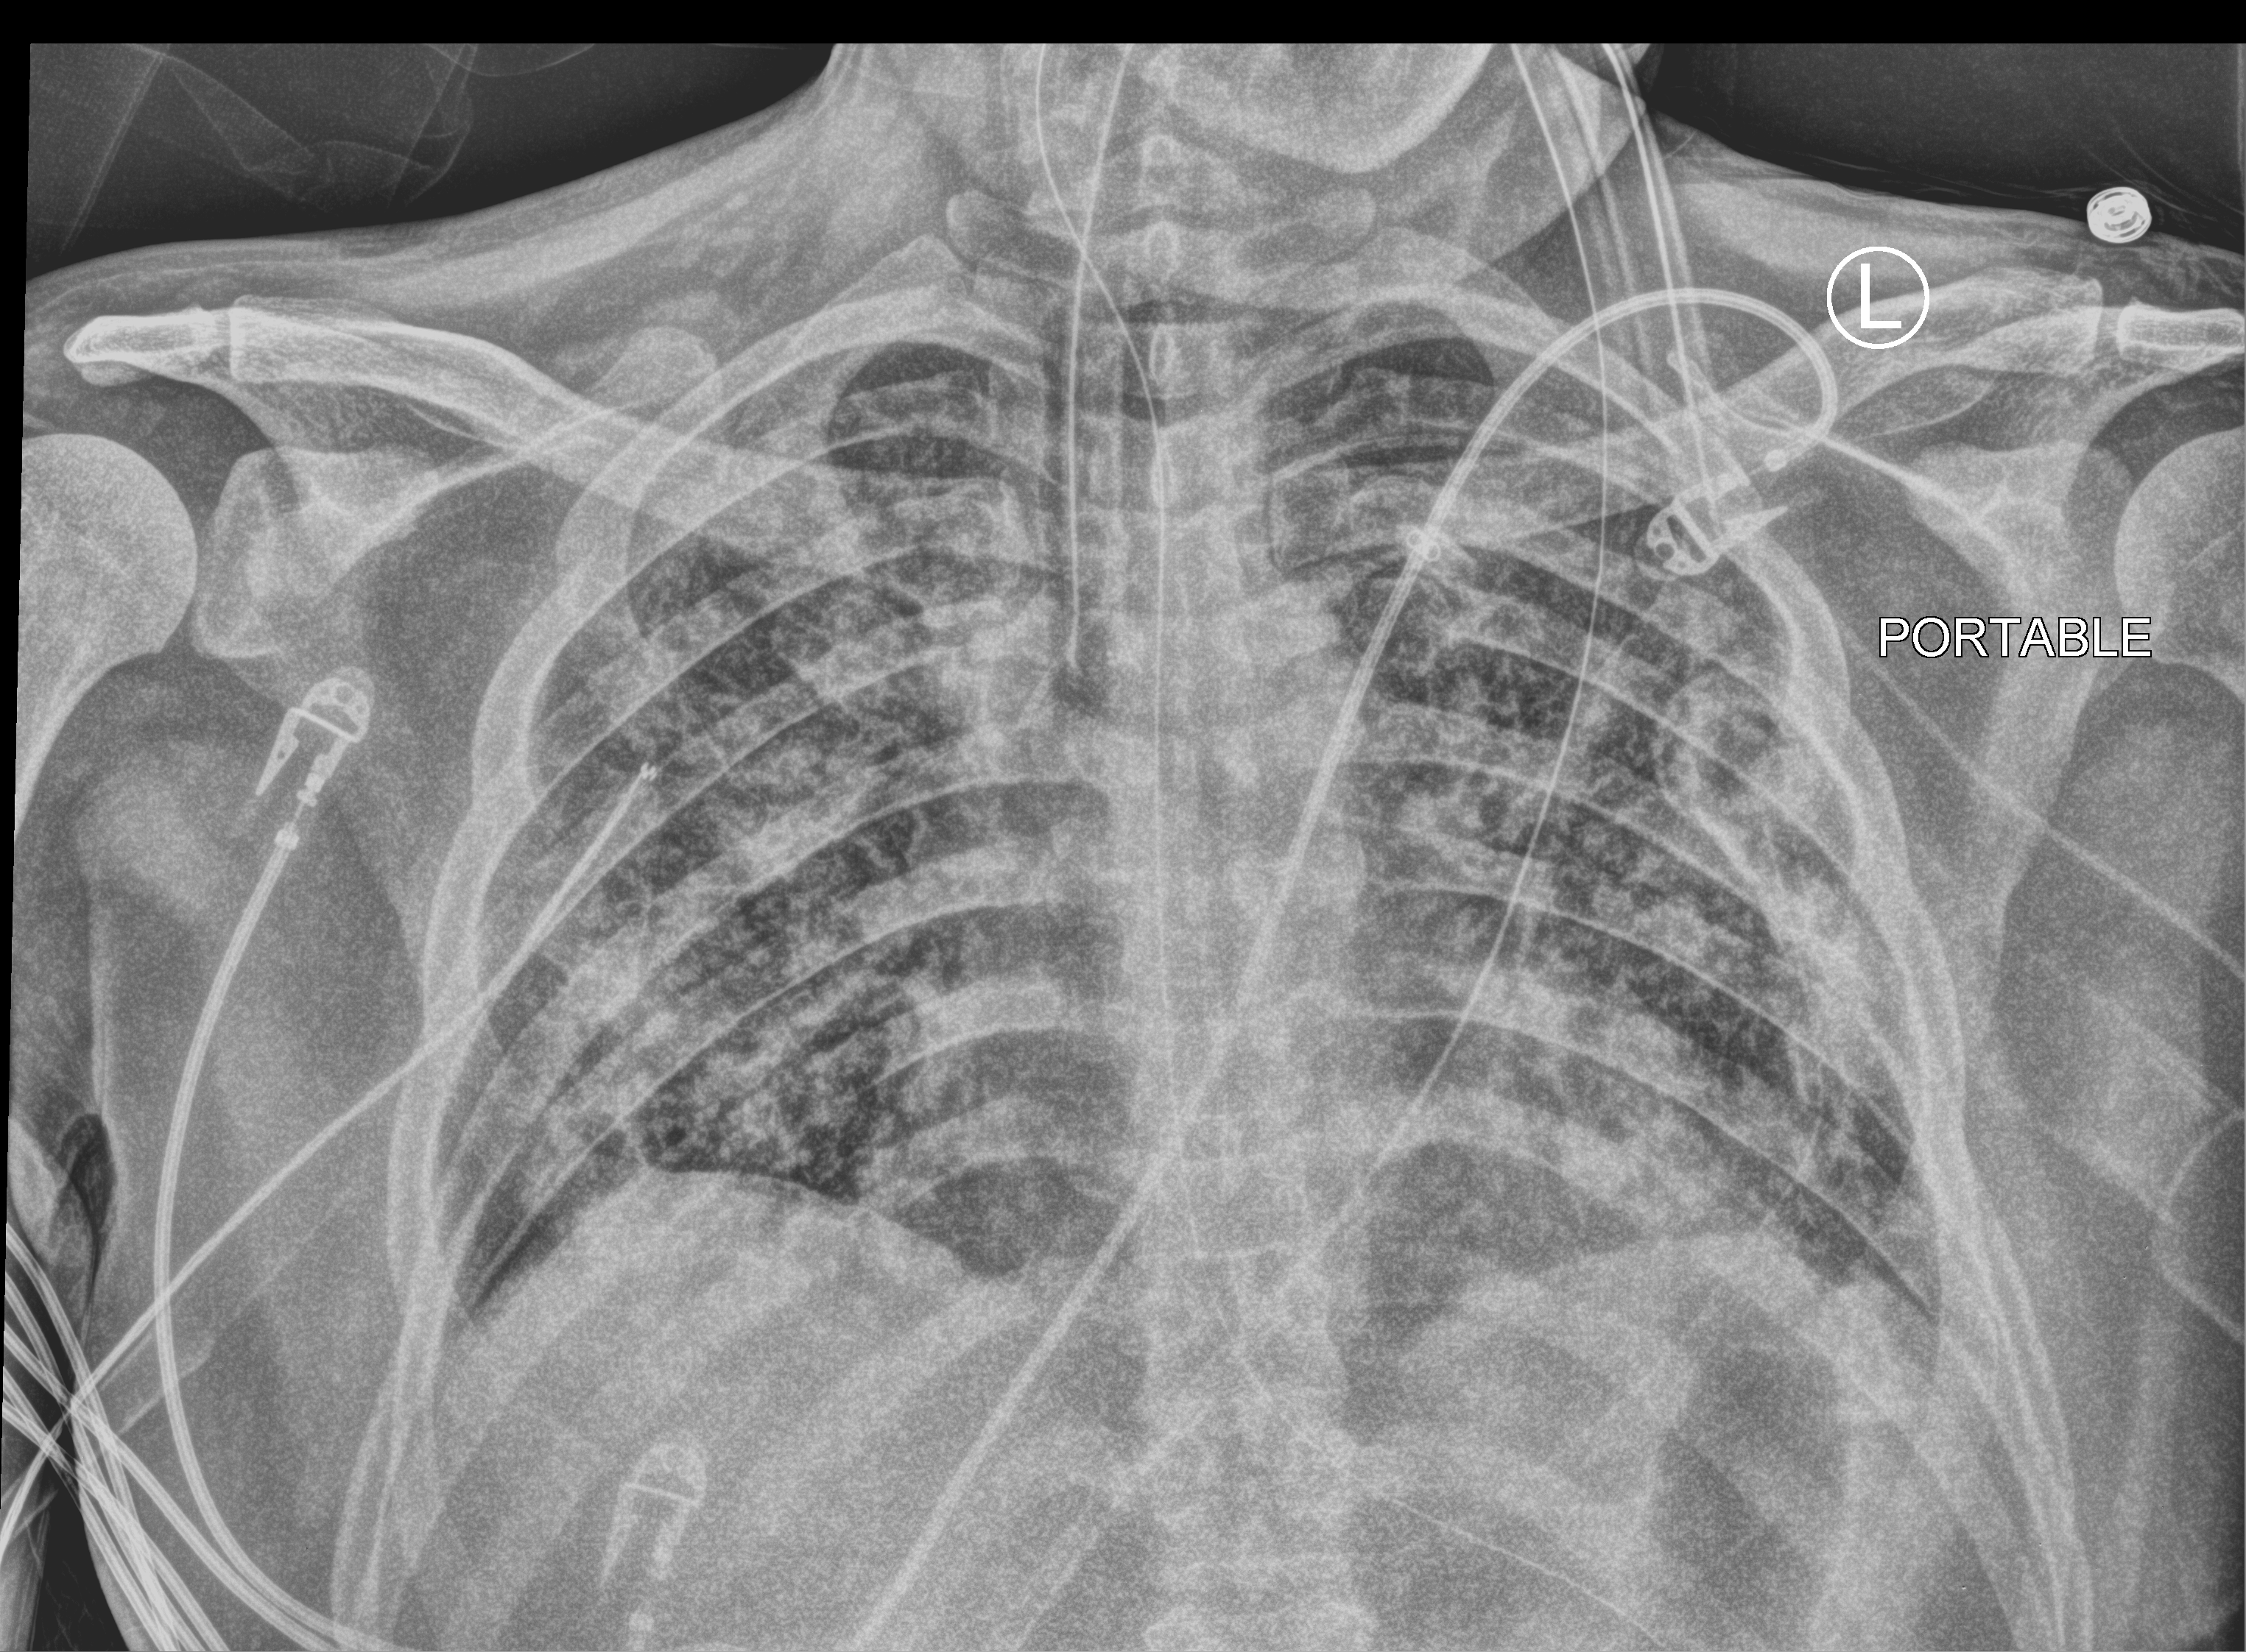
Bedside chest radiograph (computed radiography); anteroposterior (AP) projection. Patient hospitalised with COVID-19; male, aged 18–59 years.
Hospital-stay facts (about this admission, not read from this image; timing relative to this image not recorded):
- smoking status (admission record): never